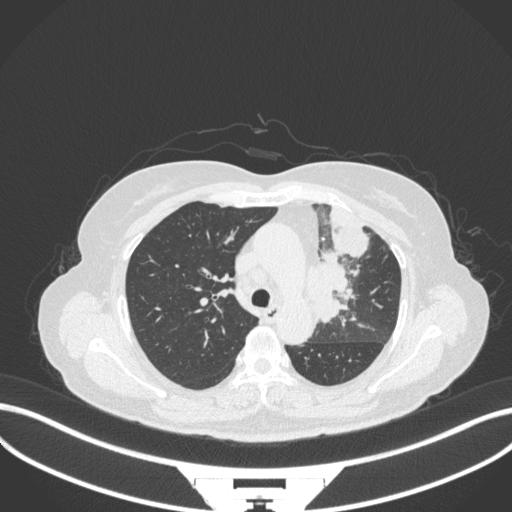
Chest CT, one axial slice; position 232 of 382 along the scan axis; reconstruction kernel B31f; 120 kVp; lung window (W 1500 / L -600 HU); 512 × 512 image matrix, field of view 400 × 400 mm. Patient: female, 64 years. From the clinical record (not read from this slice): clinical TNM (as recorded): T2a N2 M0.
Structures marked on this image (bounding box drawn by a radiologist):
- lung tumour (recorded histology: adenocarcinoma): bounding box (x1, y1, x2, y2) in pixels: (303, 250, 358, 327)
- lung tumour (recorded histology: adenocarcinoma): (329, 203, 376, 261)